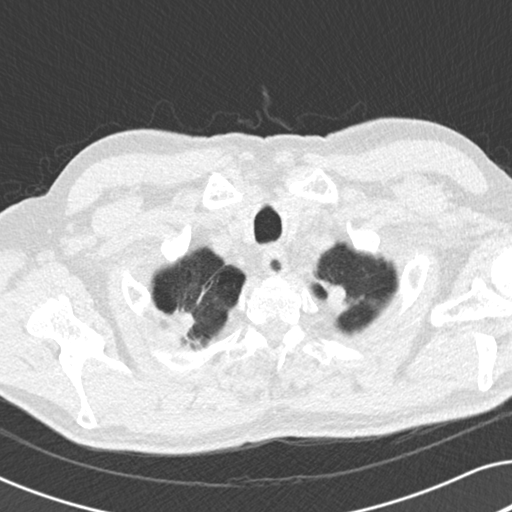
Low-dose screening chest CT, one axial slice. Position 175 of 191 along the scan axis. Reconstruction kernel B30f. Lung window (W 1500 / L -600 HU). 512 × 512 image matrix.
Outlined on this slice (expert manual segmentation):
- lesion 2 (nodule, lower lobe of right lung): bounding box (x1, y1, x2, y2) in pixels: (170, 308, 195, 336)